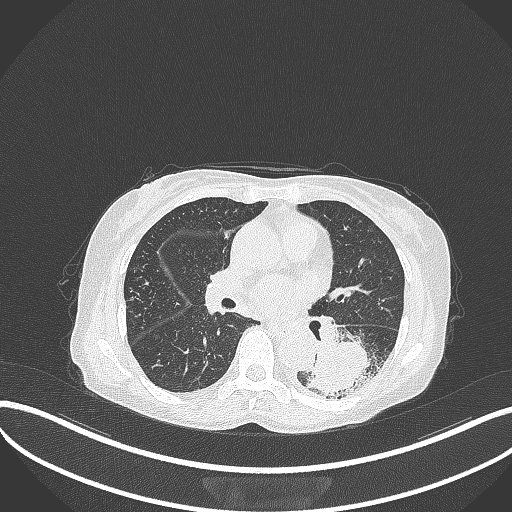
Chest CT, one axial slice. Position 163 of 370 along the scan axis. 120 kVp. Lung window (W 1500 / L -600 HU). 512 × 512 image matrix. Patient: female, 78 years. From the clinical record (not read from this slice): clinical TNM (as recorded): T3 N0 M1.
Annotated regions visible in this slice (bounding box drawn by a radiologist):
- lung tumour (recorded histology: squamous cell carcinoma): bounding box (x1, y1, x2, y2) in pixels: (308, 334, 382, 393)